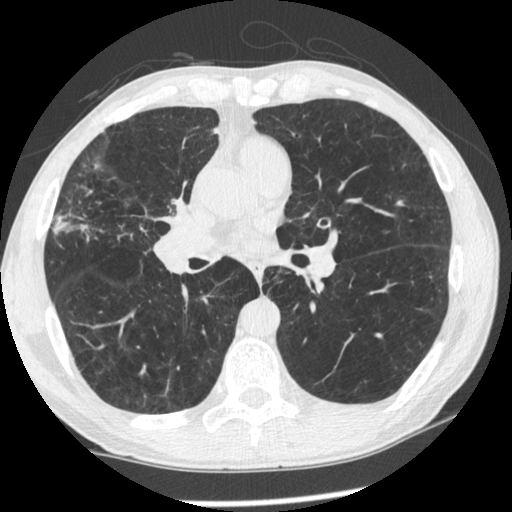
Low-dose screening chest CT, one axial slice. Slice 122 of 261 in the series (ordered by position). 120 kVp. Lung window (W 1500 / L -600 HU). 1.25 mm slice thickness. 512 × 512 image matrix, field of view 340 × 340 mm.
Annotated regions visible in this slice (manually delineated by an expert):
- lesion 1 (tumor, upper lobe of right lung): bounding box <172,197,186,213> (left, top, right, bottom; pixels)